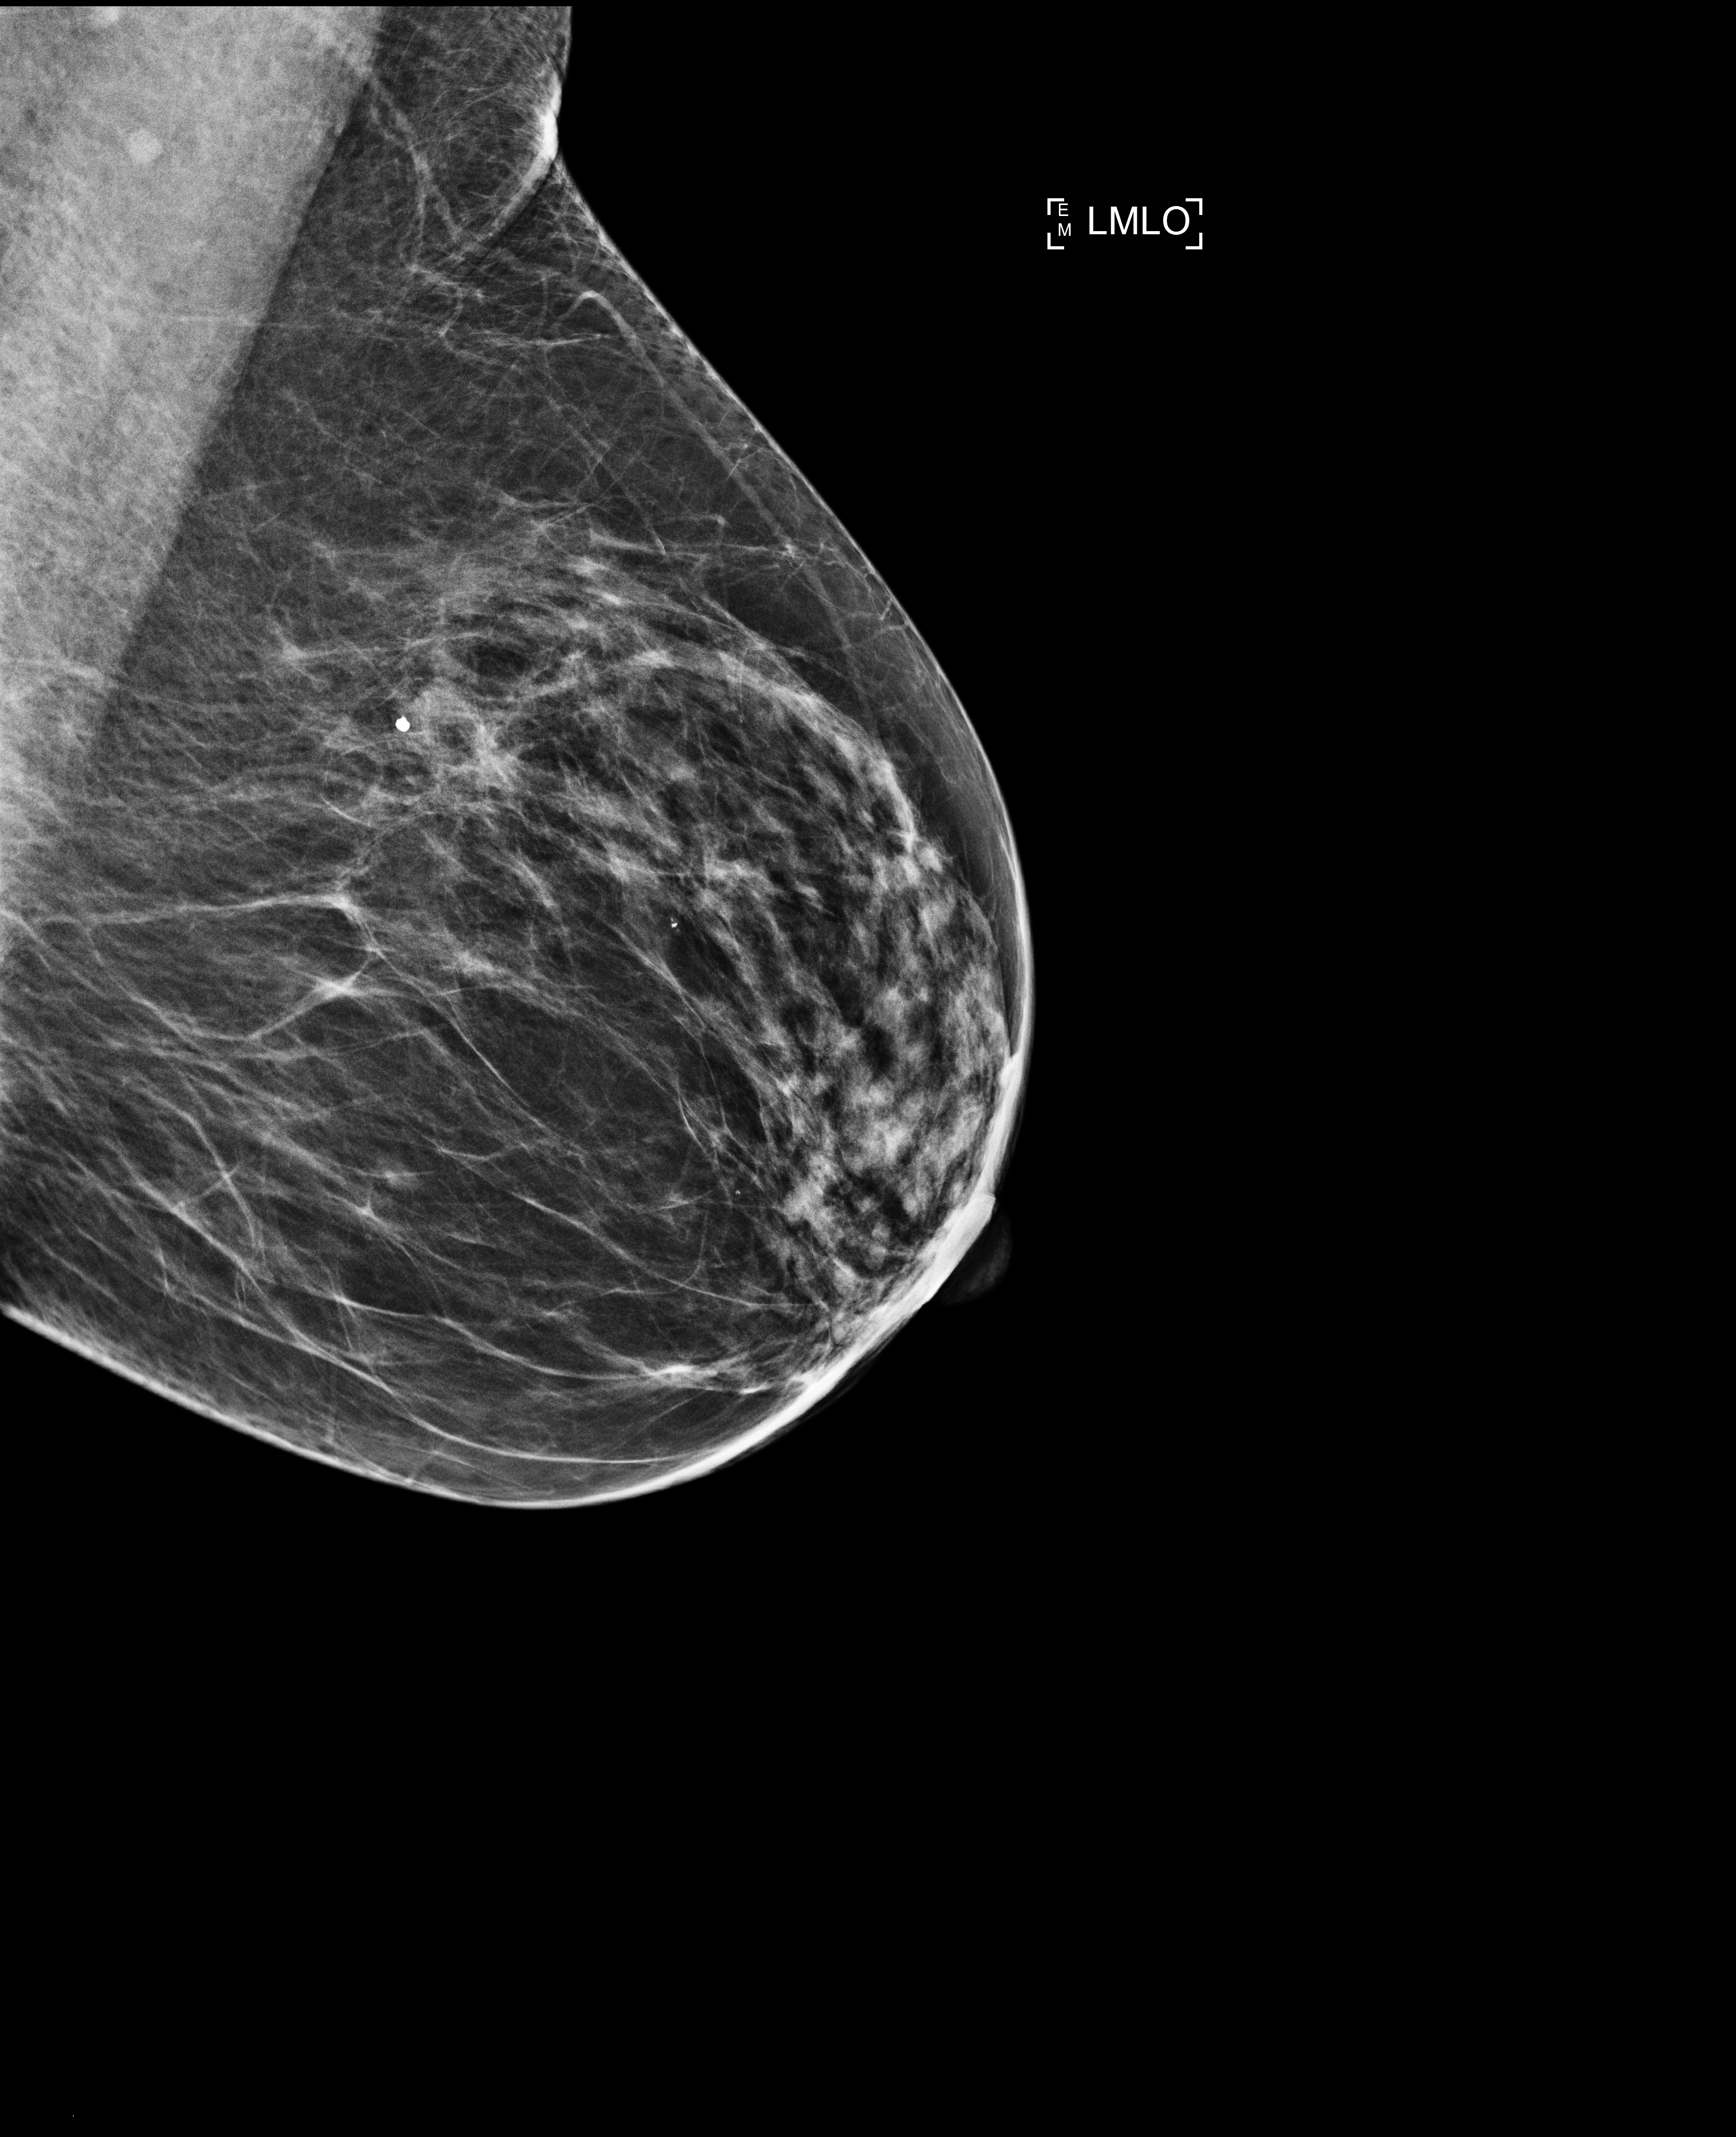
Annual screening mammography examination. Patient aged 65 years (female).
Image type: full-field digital mammogram. Breast: left. Projection: mediolateral oblique (MLO) view.